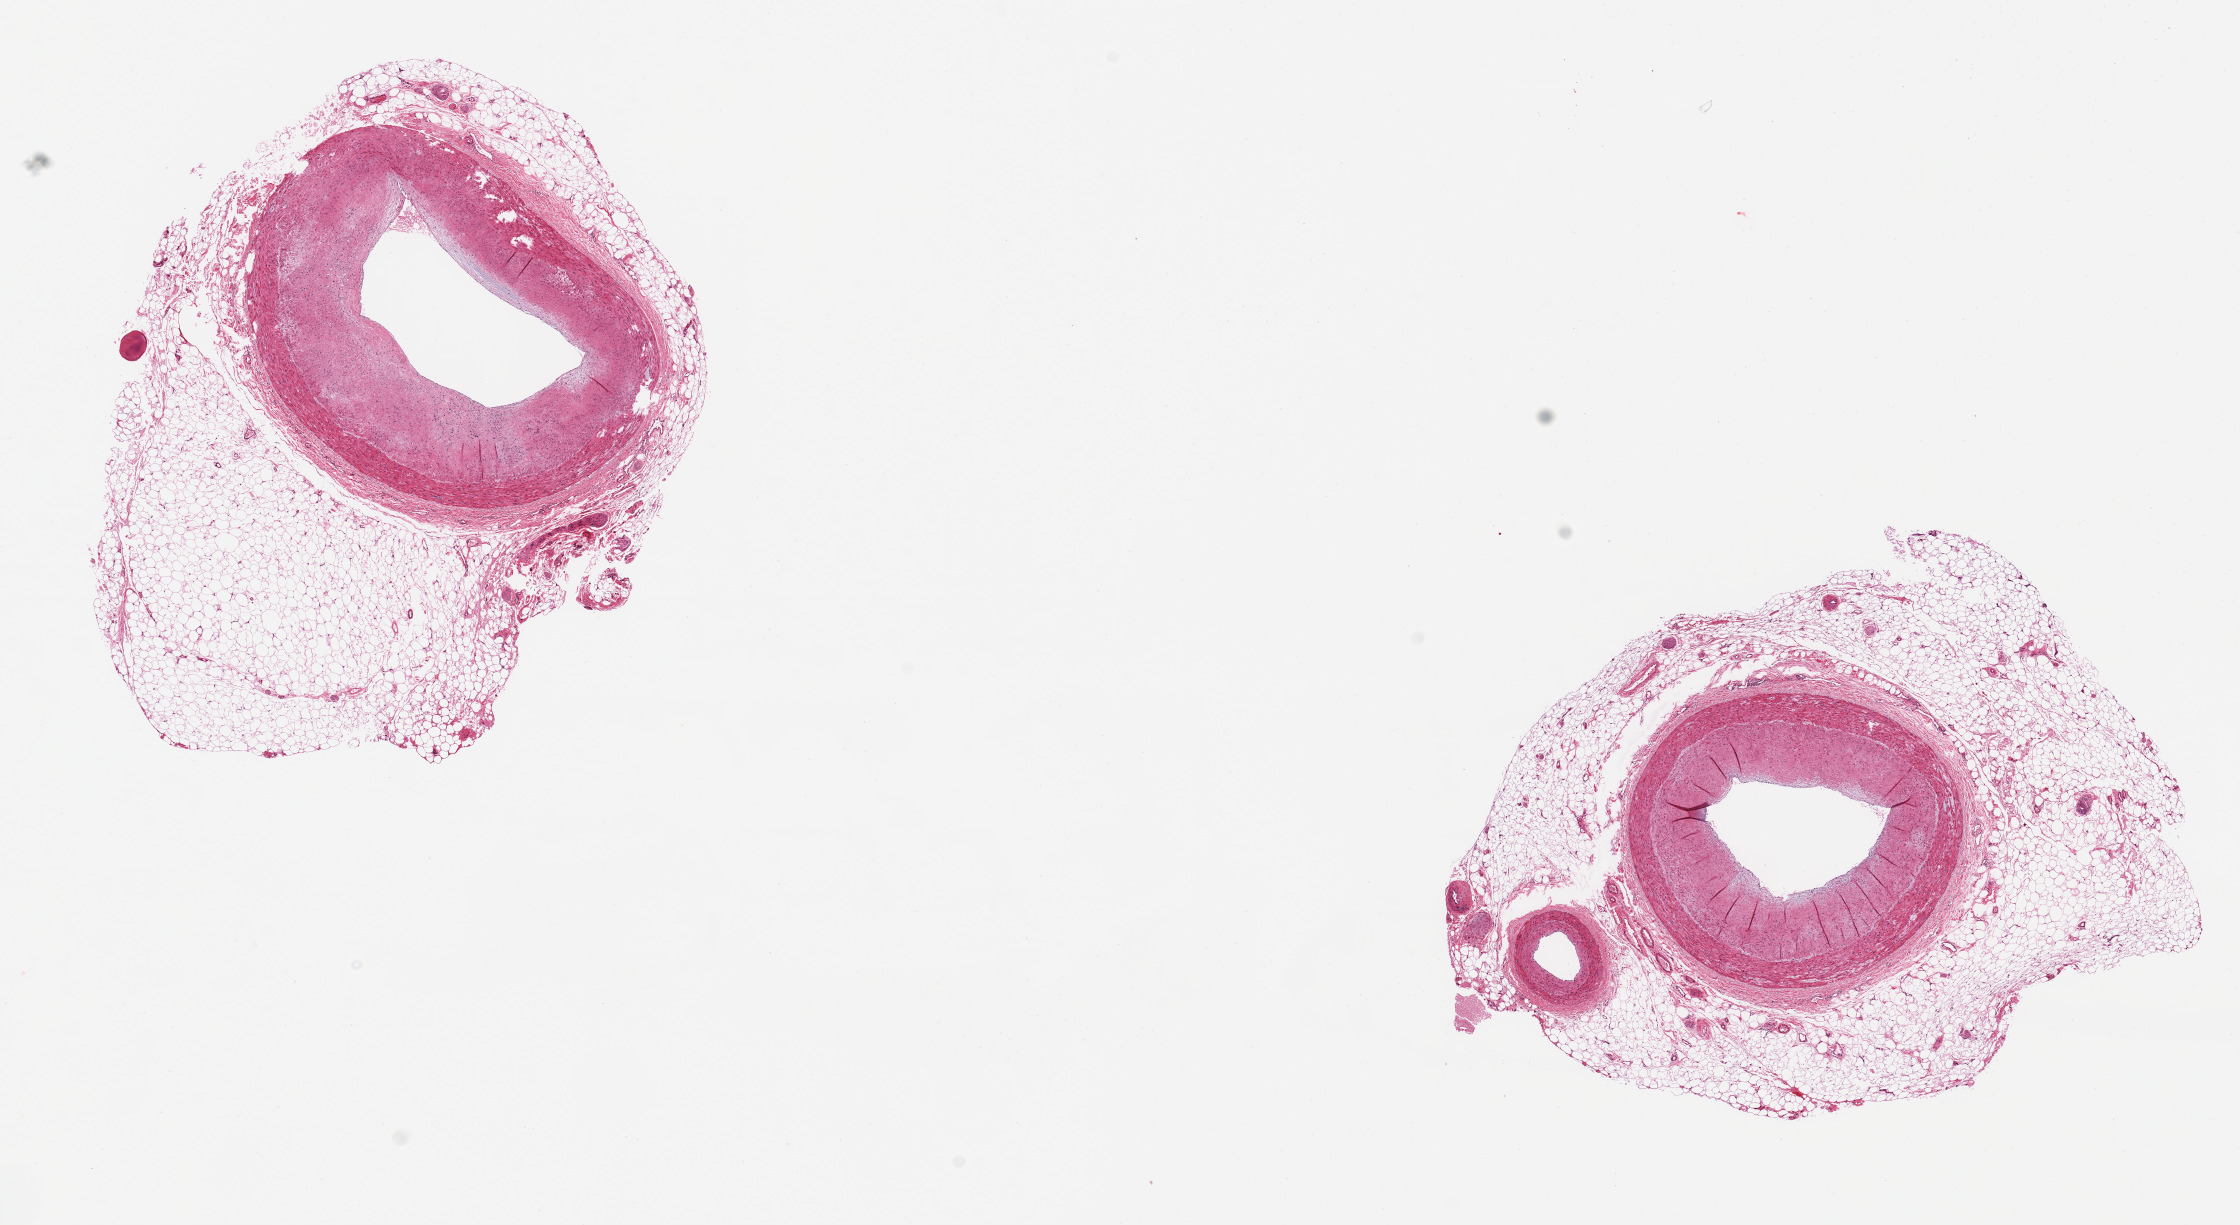
Hematoxylin and eosin (H&E) whole-slide image, a low-resolution overview of the entire scanned area, about 17.7 x 9.7 mm (from a 20x scan). PAXgene-fixed paraffin-embedded (PFPE) section. Section of coronary artery (target tissue). Tissue donor sample. Male donor.
Pathologist's review note for this sample: Moderate atherosclerosis, 50% lumen narrowed.